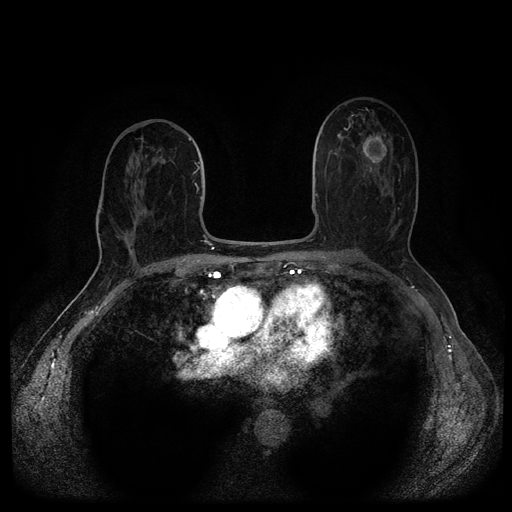
Breast MRI (dynamic contrast-enhanced, multi-phase), one axial slice; slice 56 of 116 in the series (ordered by position); dynamic contrast-enhanced series, time point 2 of 5 at this slice position (early post-contrast); 1.5 T; TE 2.6 ms, TR 5.4 ms; 512 × 512 image matrix. Female patient, age 69 years.
Annotated regions visible in this slice (semi-automatic segmentation, software-assisted and operator-edited):
- breast lesion (labelled benign in the annotation): bounding box (x1, y1, x2, y2) in pixels: (361, 132, 387, 168)